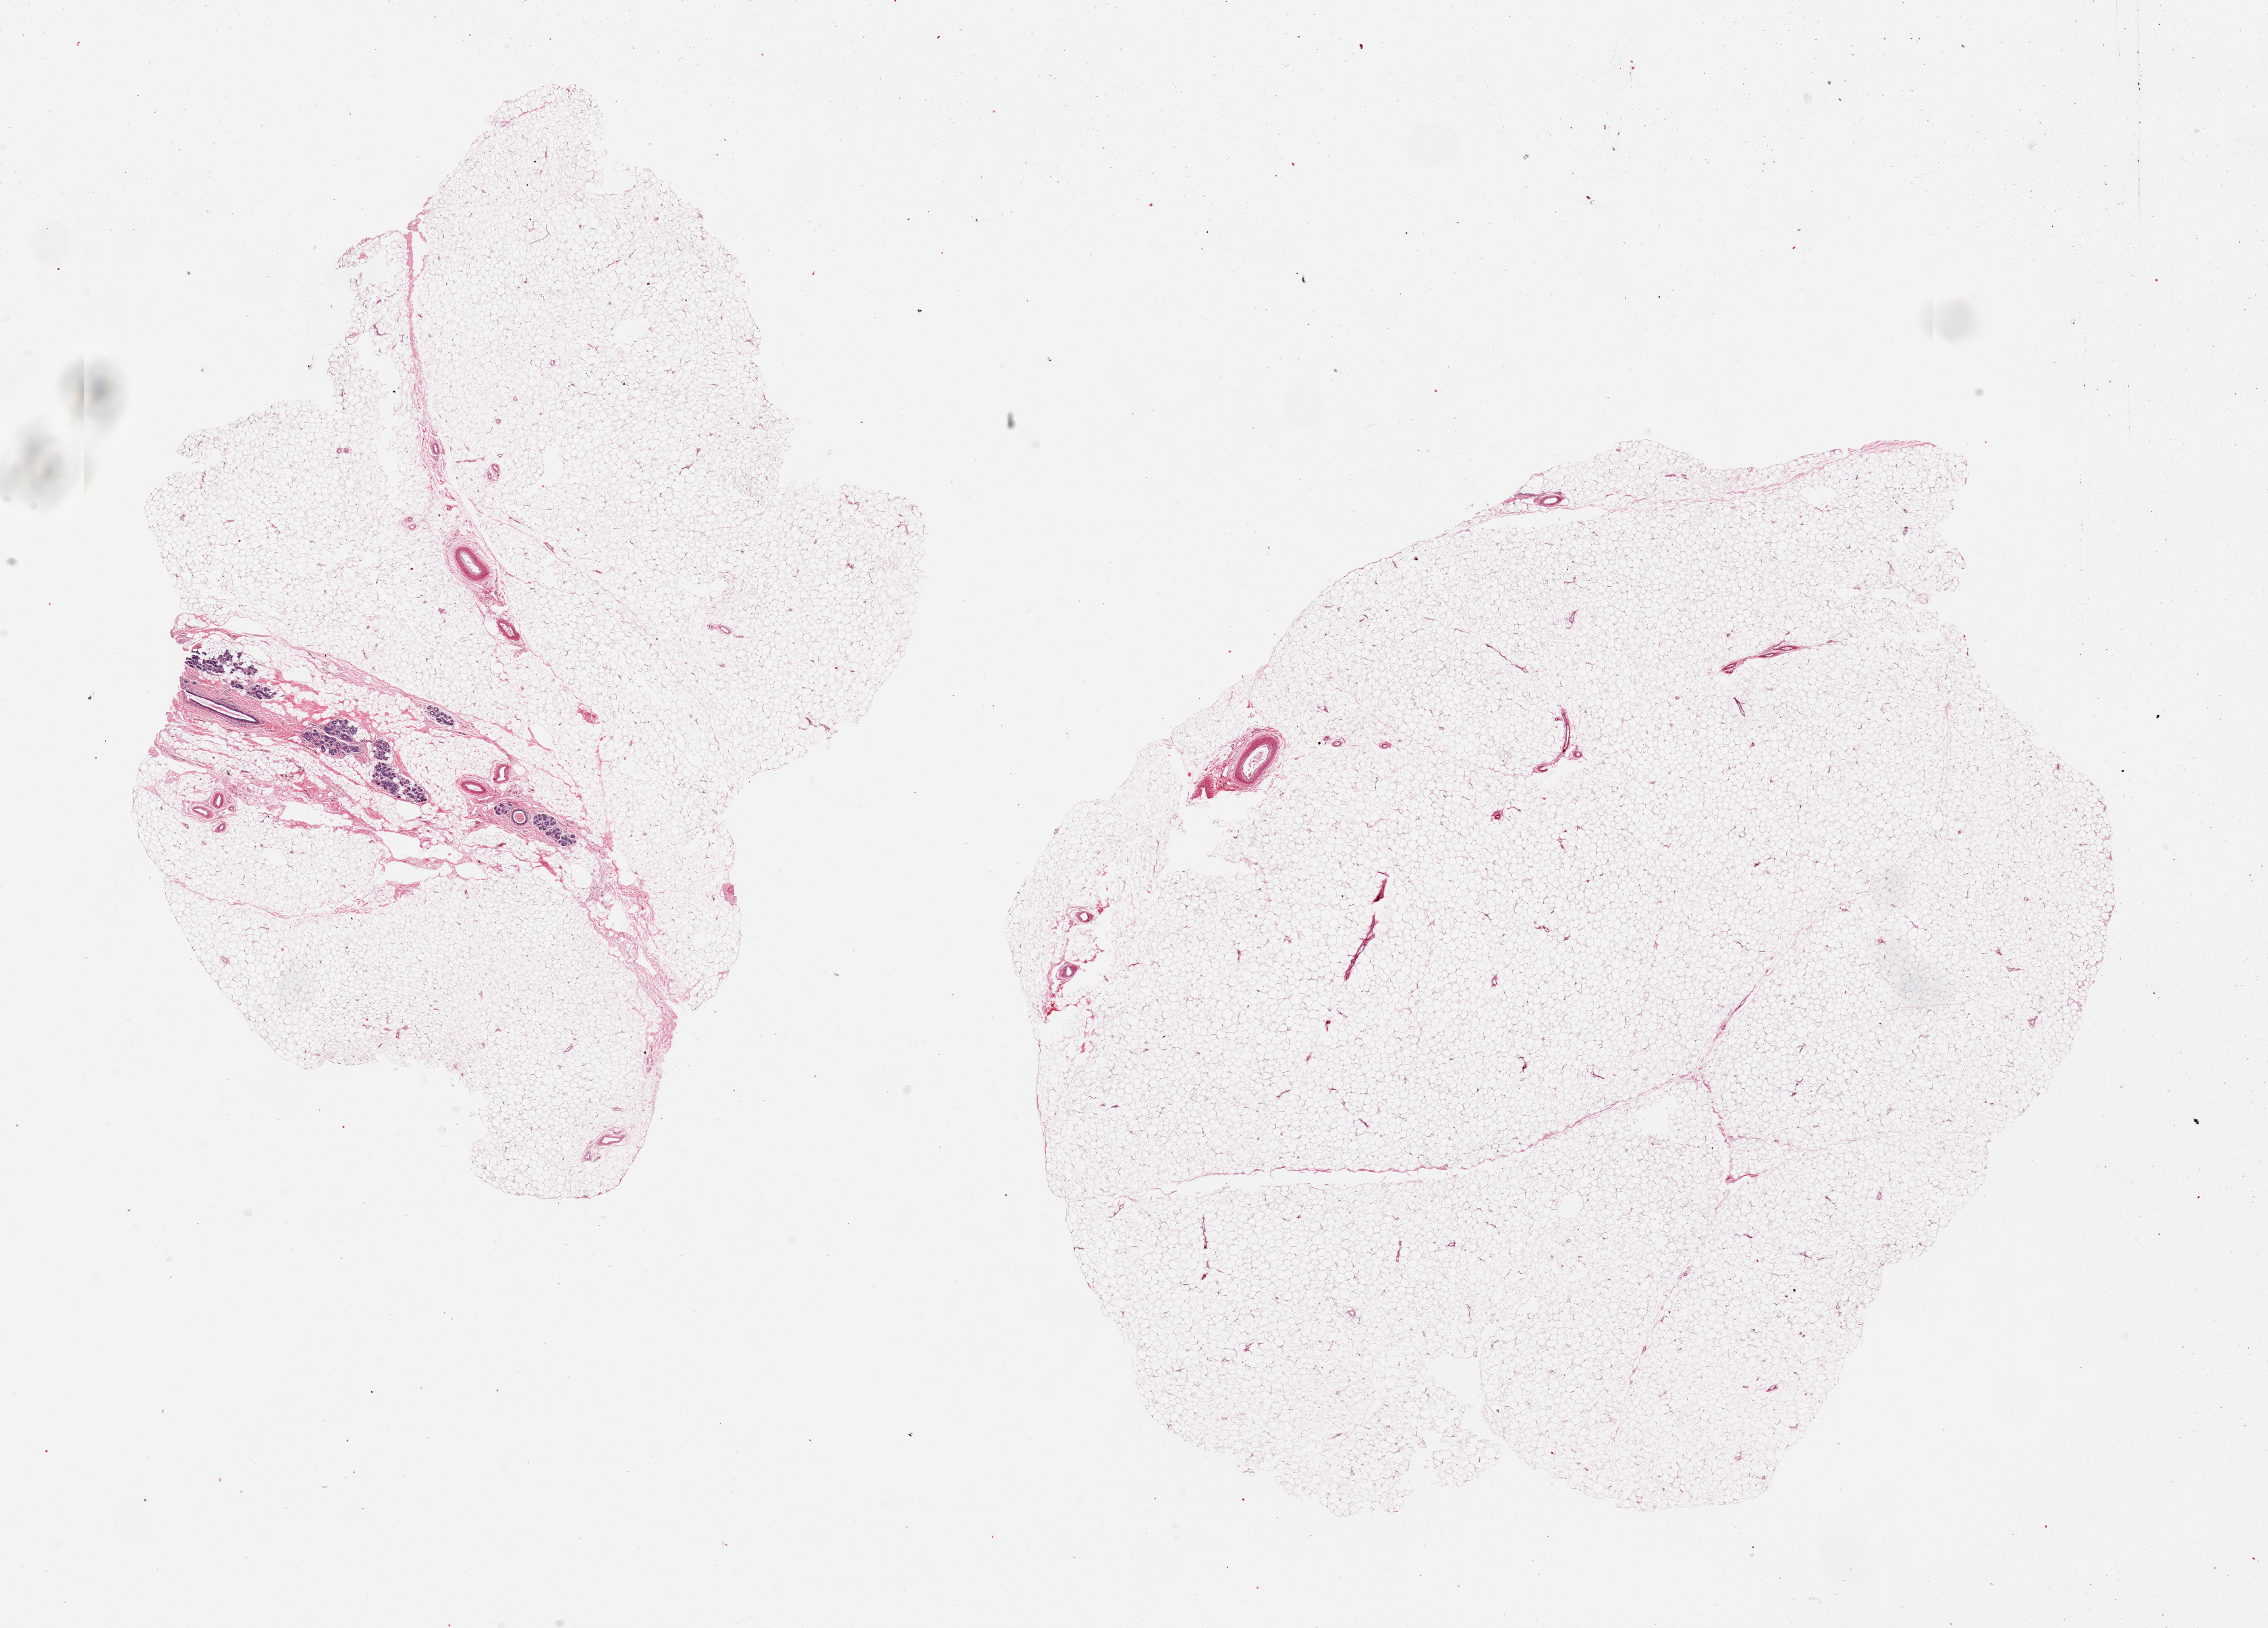
Whole-slide image, hematoxylin and eosin (H&E) stain — shown as a low-resolution overview of the whole scanned area (about 26.6 x 19.1 mm, acquisition: 20x scan). PAXgene-fixed, paraffin-embedded tissue. Target tissue: breast. Tissue donor sample. Donor sex: female.
Pathologist's review note for this sample: 2 pieces, mainly adipose tissue, trace TDLU's present, no abnormalities.